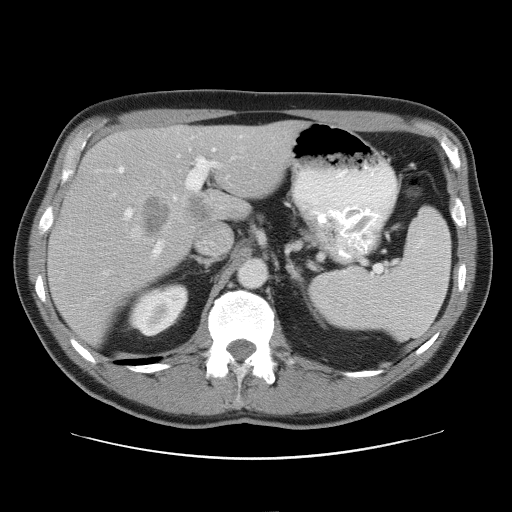
Contrast-enhanced abdominal CT, one axial slice. Slice 37 of 52 in the series (ordered by position). Intravenous contrast given. Soft-tissue window (W 400 / L 40 HU). 512 × 512 image matrix, field of view 393 × 393 mm. Male patient, age 70 years. From the clinical record (not read from this slice): diagnosis: colorectal cancer liver metastases, imaged before liver resection; multiple liver metastases: yes; largest metastasis: 4 cm; chemotherapy before resection: yes.
Outlined on this slice (manually delineated by an expert):
- hepatic veins: bounding box (x1, y1, x2, y2) in pixels: (130, 146, 244, 239)
- liver: (48, 122, 301, 343)
- planned liver remnant (the part of the liver to remain after resection): (106, 122, 301, 201)
- portal vein (with intrahepatic branches): (117, 136, 243, 259)
- liver metastasis: (188, 198, 211, 225)
- liver metastasis: (142, 199, 172, 237)